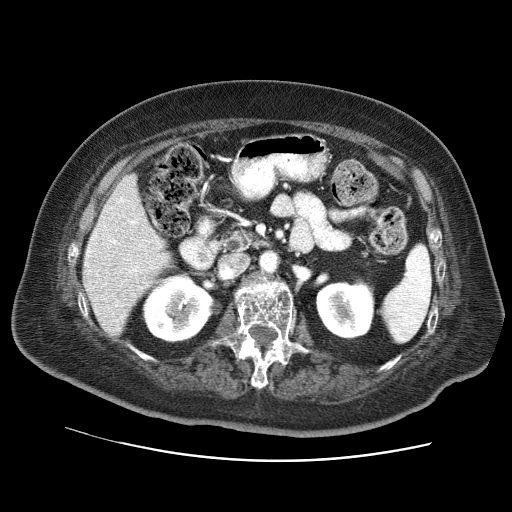
Contrast-enhanced abdominal CT (liver protocol), one axial slice. Slice 28 of 73 in the series (ordered by position). Soft-tissue window (W 400 / L 40 HU). 2.5 mm slice thickness. 512 × 512 image matrix, field of view 380 × 380 mm. From the clinical record (not read from this slice): diagnosis: hepatocellular carcinoma (patient treated with transarterial chemoembolisation; whether this scan precedes or follows treatment is not stated here); TNM stage (as recorded): Stage-I.
Annotated regions visible in this slice (semi-automatic segmentation, software-assisted and operator-edited):
- liver parenchyma outside the tumour (the mass and vessels are separate outlines, so this box may not span the whole liver): box from (x=84, y=174) to (x=168, y=322) px
- liver vessels: (x=86, y=197)–(x=153, y=321)